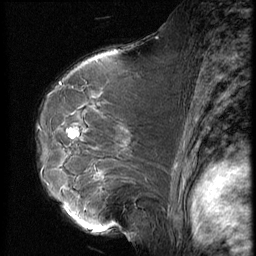
Breast MRI (dynamic contrast-enhanced), one sagittal slice. Slice 42 of 62 in the series (ordered by position). 3 images stored at this slice position (order not interpretable as contrast timing). 1.5 T. TE 4.2 ms, TR 9 ms. 2.5 mm slice thickness. 256 × 256 image matrix, field of view 180 × 180 mm. Patient: female, 50 years. From the clinical record (not read from this slice): setting: breast cancer imaged before/during neoadjuvant chemotherapy; receptor status: HR-positive, HER2-negative.
Outlined on this slice (semi-automatic segmentation, software-assisted and operator-edited):
- analysis volume of interest (the breast-tissue region the enhancement analysis was run in; not a lesion): bounding box [x1, y1, x2, y2] px = [59, 125, 139, 238]
- tumour enhancement mask (voxels above the 140 % enhancement threshold inside the analysis volume of interest): [71, 132, 78, 137]